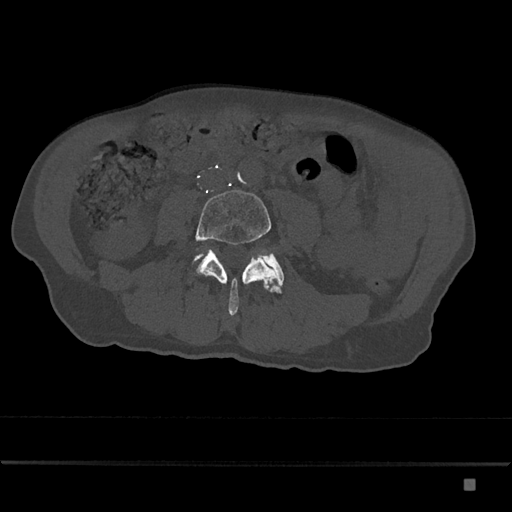
CT including the spine, one axial slice; slice 328 of 797 in the series (ordered by position); bone window (W 1800 / L 400 HU); 0.5 mm slice thickness; 512 × 512 image matrix. Male patient, age 72 years. Case-level facts recorded for this patient, not image findings: primary cancer: prostate.
Structures marked on this image (semi-automatic segmentation, software-assisted and operator-edited):
- L4 vertebra: bounding box (x1, y1, x2, y2) in pixels: (195, 190, 282, 316)
- L5 vertebra: (194, 250, 284, 294)